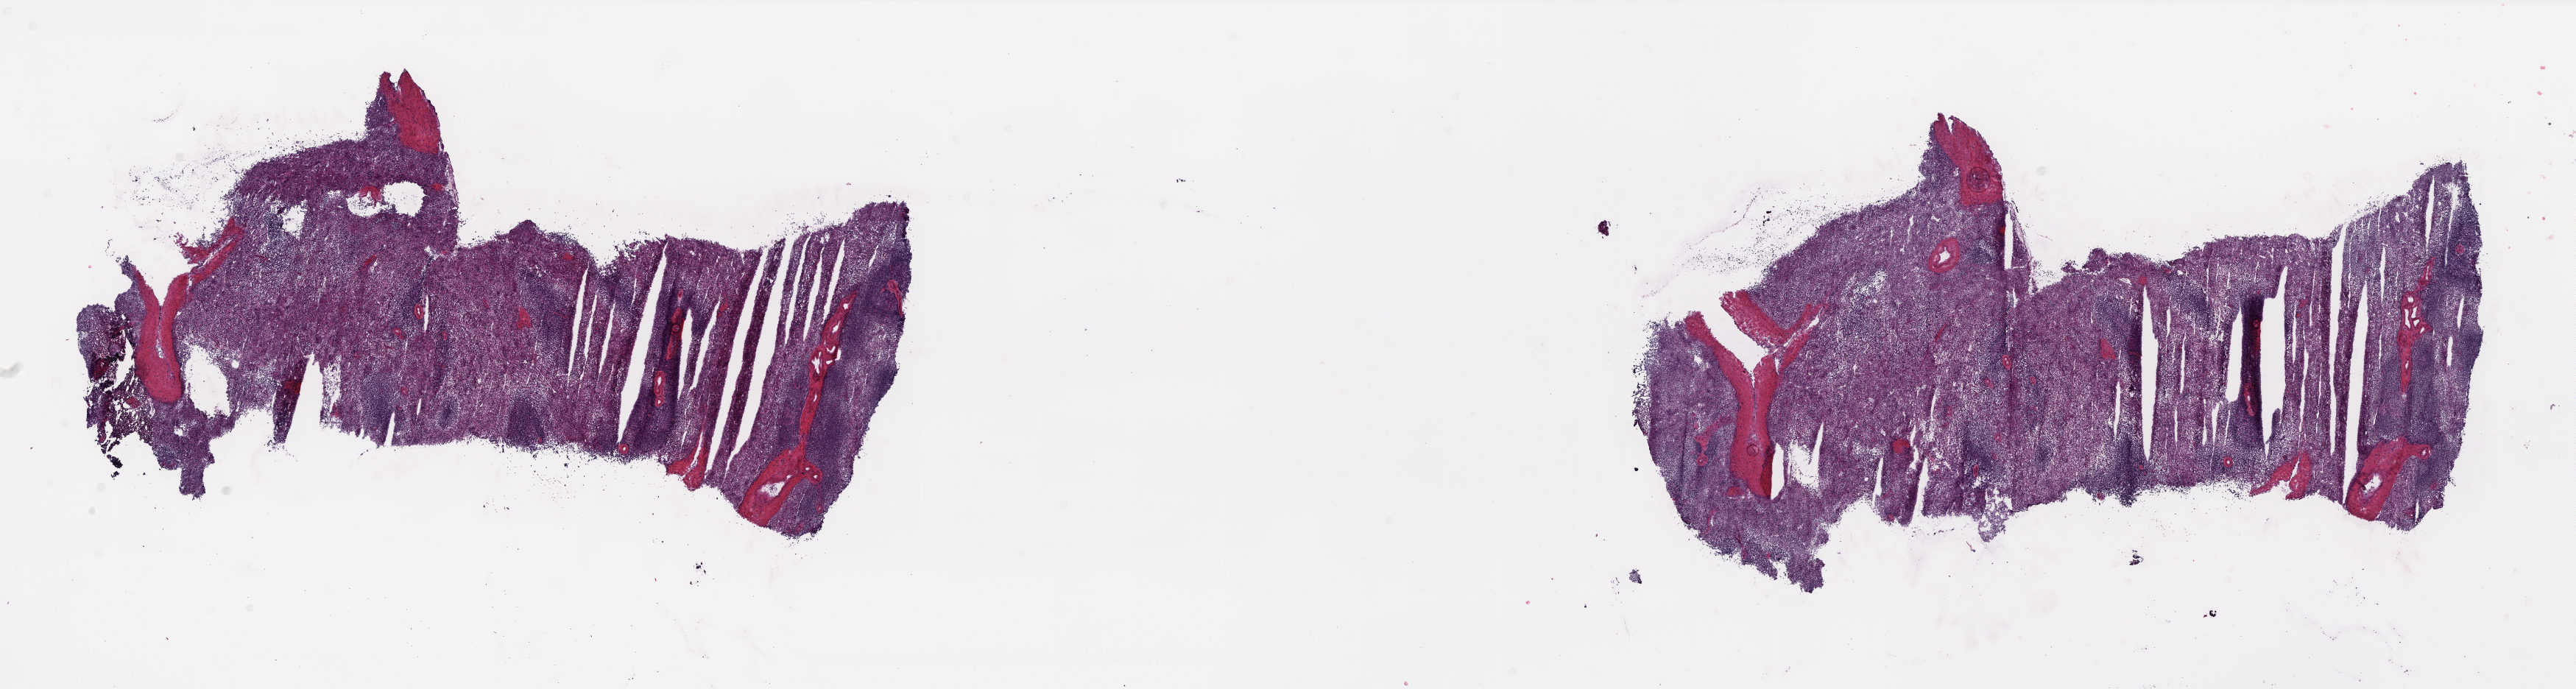
Digitized Hematoxylin and eosin (H&E) stained tissue section (whole slide) — whole scanned area (about 27.9 x 7.5 mm) shown as a low-resolution overview, frozen section, pancreas, solid tissue normal (non-tumour tissue) sample. Patient sex: female. Pathologist review of this section (percent, as recorded): tumour cells 0%, tumour nuclei 0%, normal cells 100%, stromal cells 0%, necrosis 0%. Inflammatory infiltration, as recorded: lymphocyte infiltration 8%, monocyte infiltration 0%, neutrophil infiltration 0%.
* this section: solid tissue normal (non-tumour) sample from the same patient
* patient diagnosis: Adenocarcinoma, NOS (tail of pancreas)